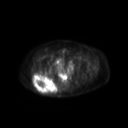
FDG PET of an extremity soft-tissue mass (from a PET/CT study), one axial slice; slice 57 of 267 in the series (ordered by position); 3.27 mm slice thickness; 128 × 128 image matrix. Female patient, age 60 years. From the clinical record (not read from this slice): histological type: spindle cell suggestive of myxofibrosarcoma; grade: intermediate; site of the primary tumour: right buttock.
Structures marked on this image (expert contour drawn on MRI and transferred to this co-registered scan by the dataset authors):
- gross tumour volume (mass): box from (x=33, y=73) to (x=57, y=95) px